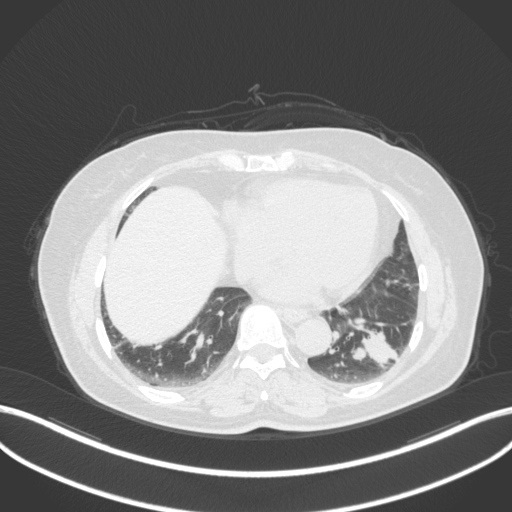
Chest CT, one axial slice; slice 127 of 307 in the series (ordered by position); reconstruction kernel B31f; 120 kVp; lung window (W 1500 / L -600 HU); 1 mm slice thickness; 512 × 512 image matrix. Patient: female, 59 years. Case-level facts recorded for this patient, not image findings: clinical TNM (as recorded): T2a N0 M0.
Outlined on this slice (bounding box drawn by a radiologist):
- lung tumour (recorded histology: adenocarcinoma): bounding box [x1, y1, x2, y2] px = [344, 328, 405, 372]